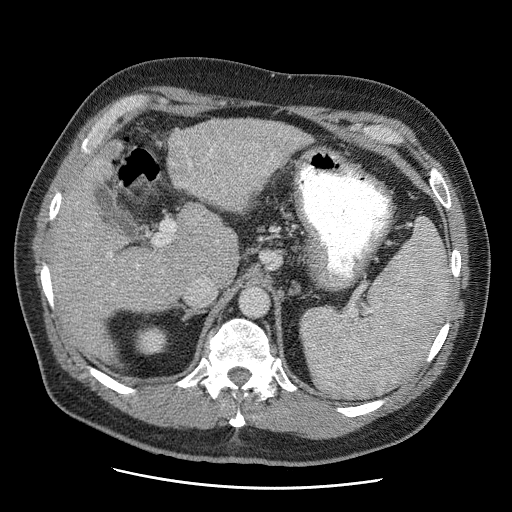
Contrast-enhanced abdominal CT (liver protocol), one axial slice. Position 31 of 81 along the scan axis. Soft-tissue window (W 400 / L 40 HU). 512 × 512 image matrix, field of view 380 × 380 mm. From the clinical record (not read from this slice): diagnosis: hepatocellular carcinoma (patient treated with transarterial chemoembolisation; whether this scan precedes or follows treatment is not stated here); TNM stage (as recorded): Stage-IIIA; Child-Pugh class: A; tumour differentiation: moderately differentiated; tumour nodularity: multinodular.
Outlined on this slice (semi-automatically segmented with operator editing):
- abdominal aorta: box from (x=239, y=288) to (x=268, y=317) px
- liver parenchyma outside the tumour (the mass and vessels are separate outlines, so this box may not span the whole liver): (x=48, y=118)–(x=310, y=356)
- liver vessels: (x=210, y=149)–(x=212, y=151)